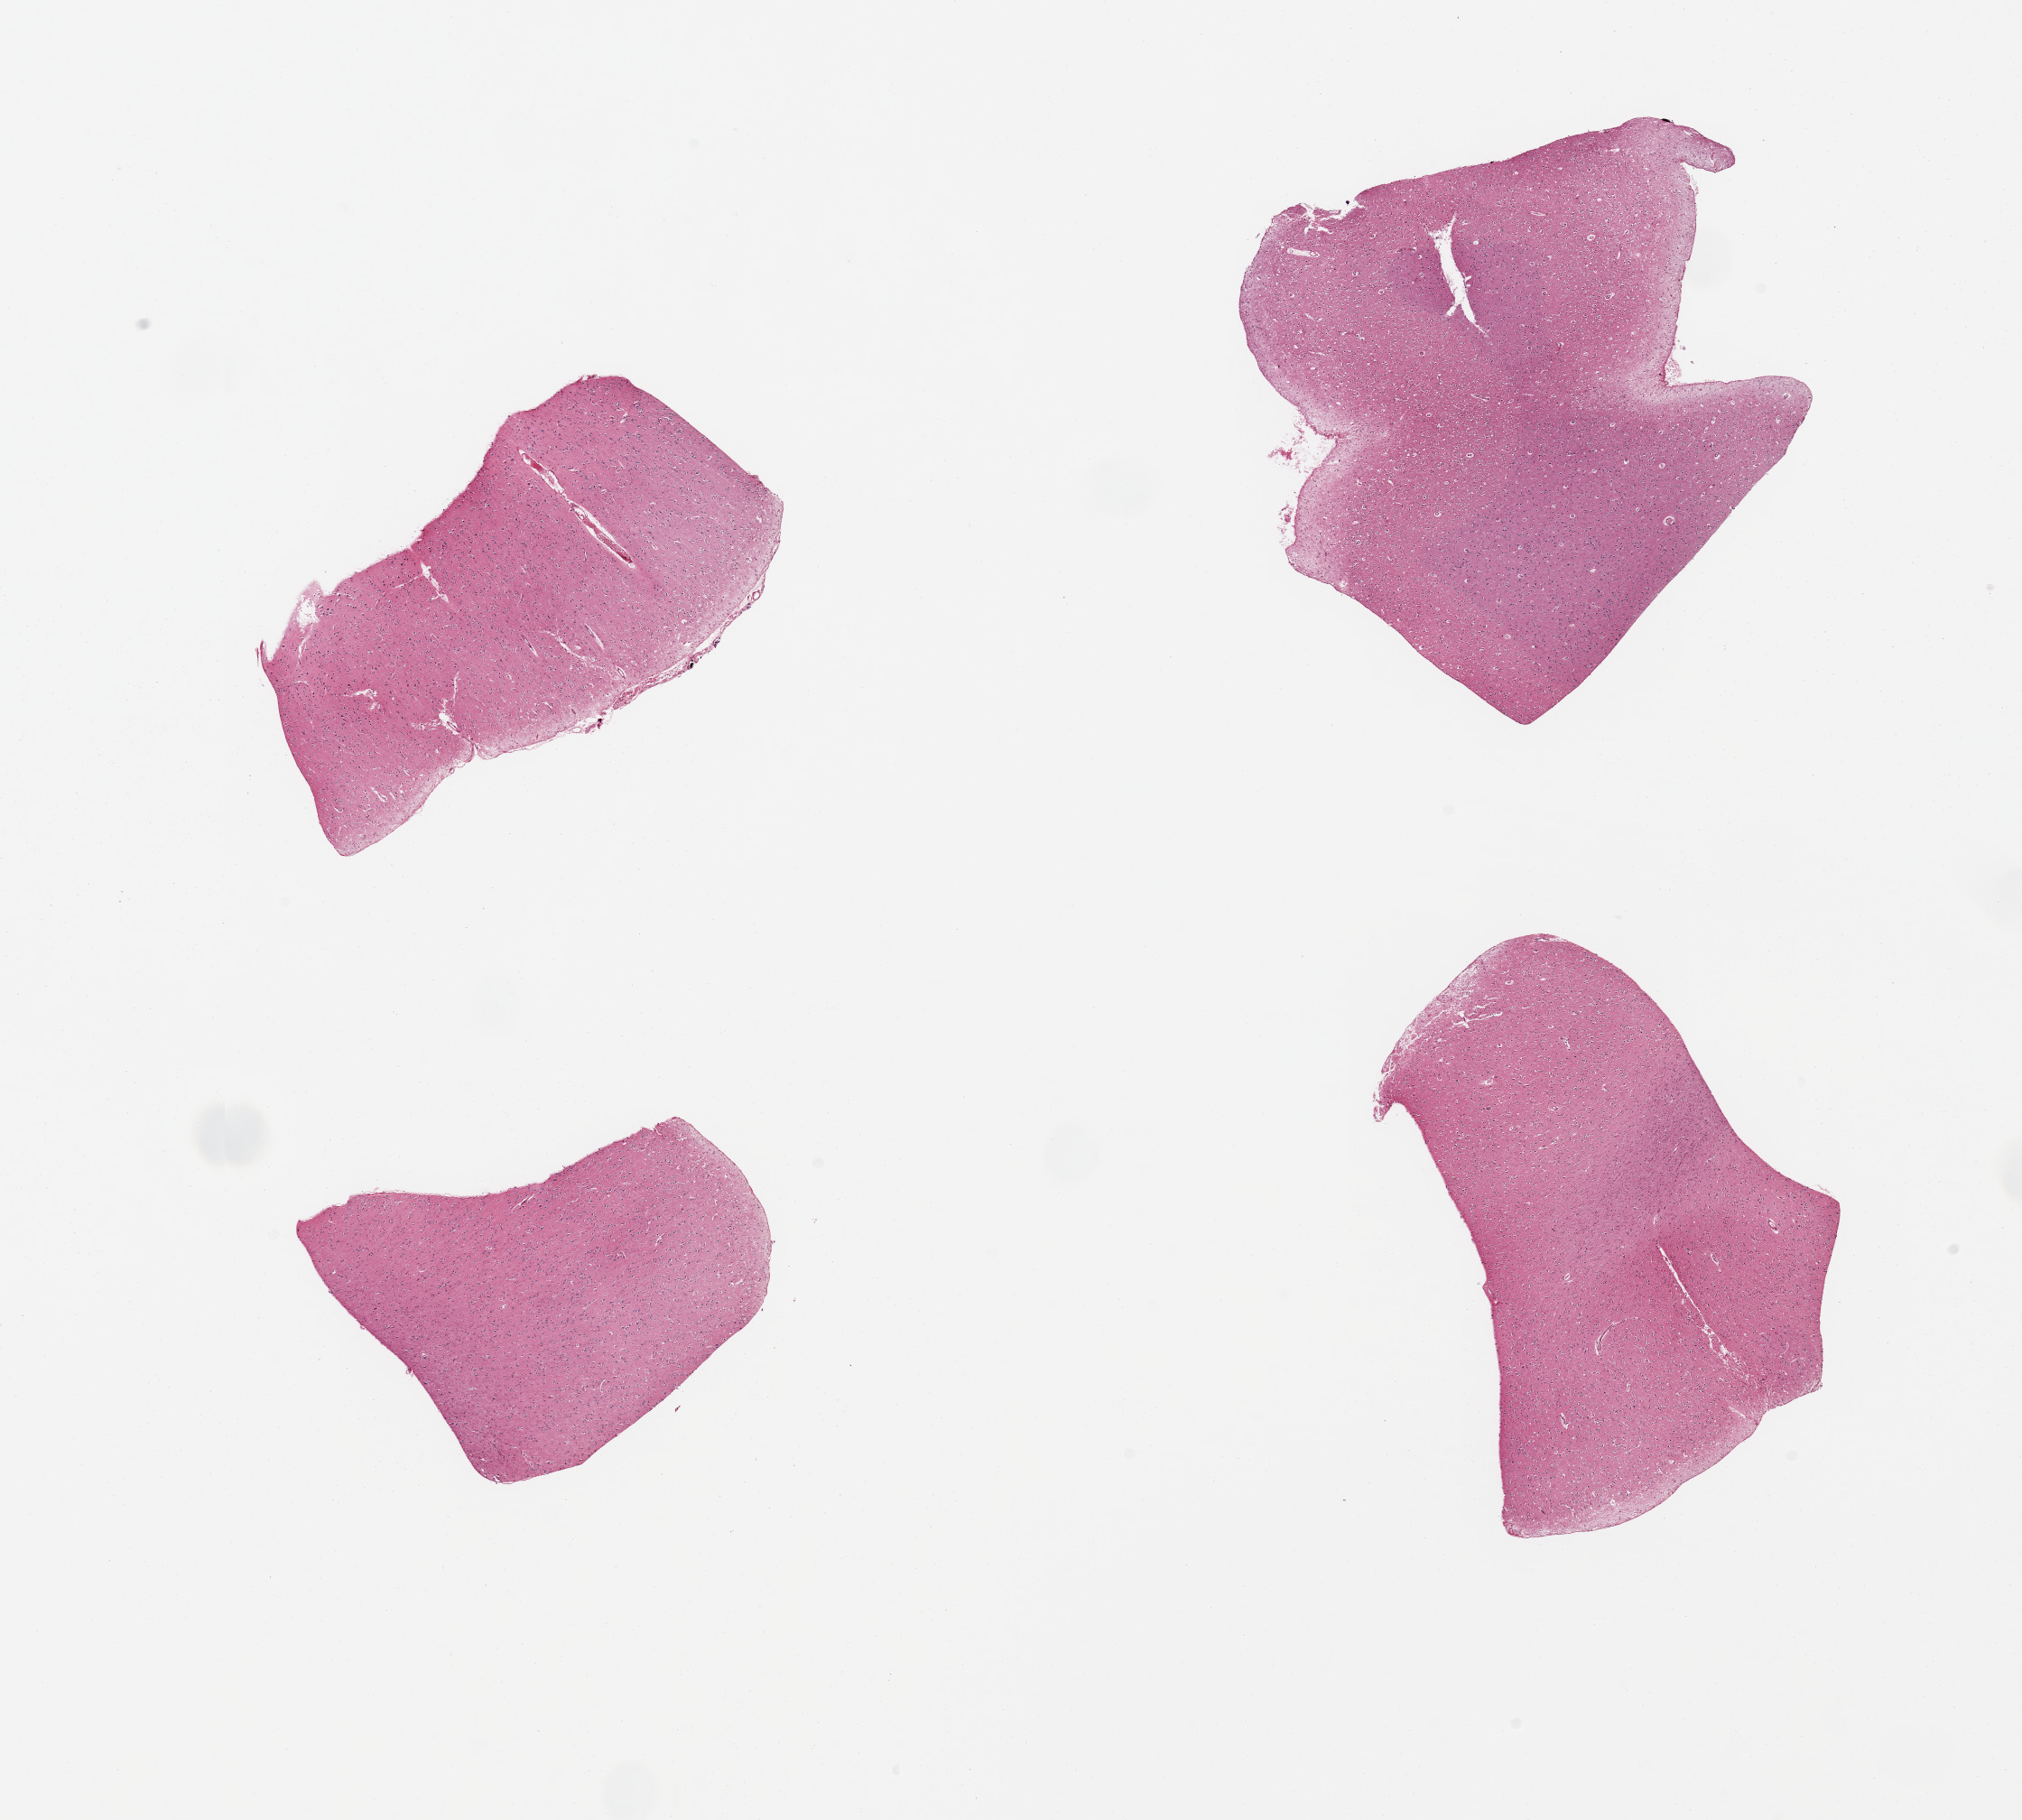
Whole-slide image, hematoxylin and eosin (H&E) stain — a low-resolution overview of the entire scanned area, about 17.7 x 15.9 mm; PAXgene-fixed paraffin-embedded (PFPE) section; sampled site (target tissue): cerebral cortex; donor tissue sample. Donor: male.
Review note (as recorded): 4 pieces; mild to moderate autolysis.